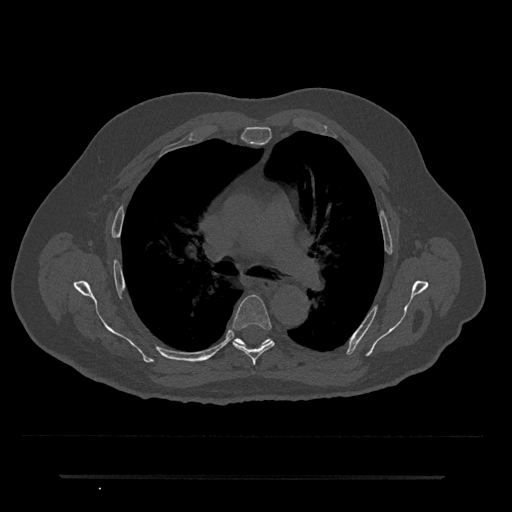
CT including the spine, one axial slice. Slice 472 of 797 in the series (ordered by position). Reconstruction kernel Br40s/3. 120 kVp. Bone window (W 1800 / L 400 HU). 512 × 512 image matrix, field of view 437 × 437 mm. Male patient, age 69 years. Case-level facts recorded for this patient, not image findings: primary cancer: prostate.
Structures marked on this image (semi-automatically segmented with operator editing):
- T5 vertebra: box from (x=232, y=295) to (x=275, y=365) px
- T6 vertebra: (x=236, y=339)–(x=242, y=344)